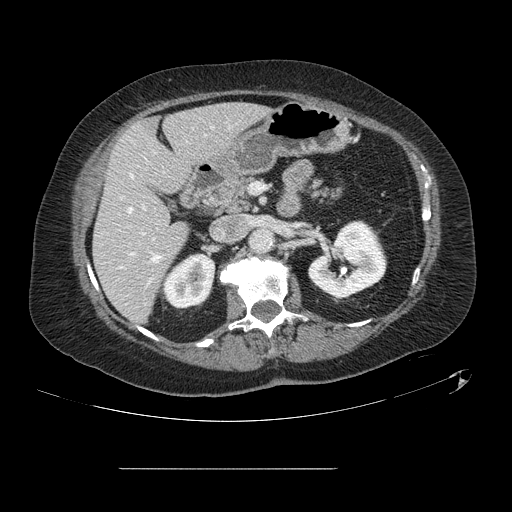
Contrast-enhanced abdominal CT, one axial slice; slice 59 of 148 in the series (ordered by position); intravenous contrast given; soft-tissue window (W 400 / L 40 HU); 512 × 512 image matrix, field of view 439 × 439 mm. Female patient, age 75 years. Case-level facts recorded for this patient, not image findings: diagnosis: colorectal cancer liver metastases, imaged before liver resection; multiple liver metastases: no; largest metastasis: 2.4 cm; disease in both lobes: no.
Structures marked on this image (manually delineated by an expert):
- hepatic veins: bounding box (x1, y1, x2, y2) in pixels: (128, 175, 161, 262)
- liver: (94, 104, 267, 322)
- planned liver remnant (the part of the liver to remain after resection): (94, 104, 268, 322)
- portal vein (with intrahepatic branches): (132, 207, 145, 255)